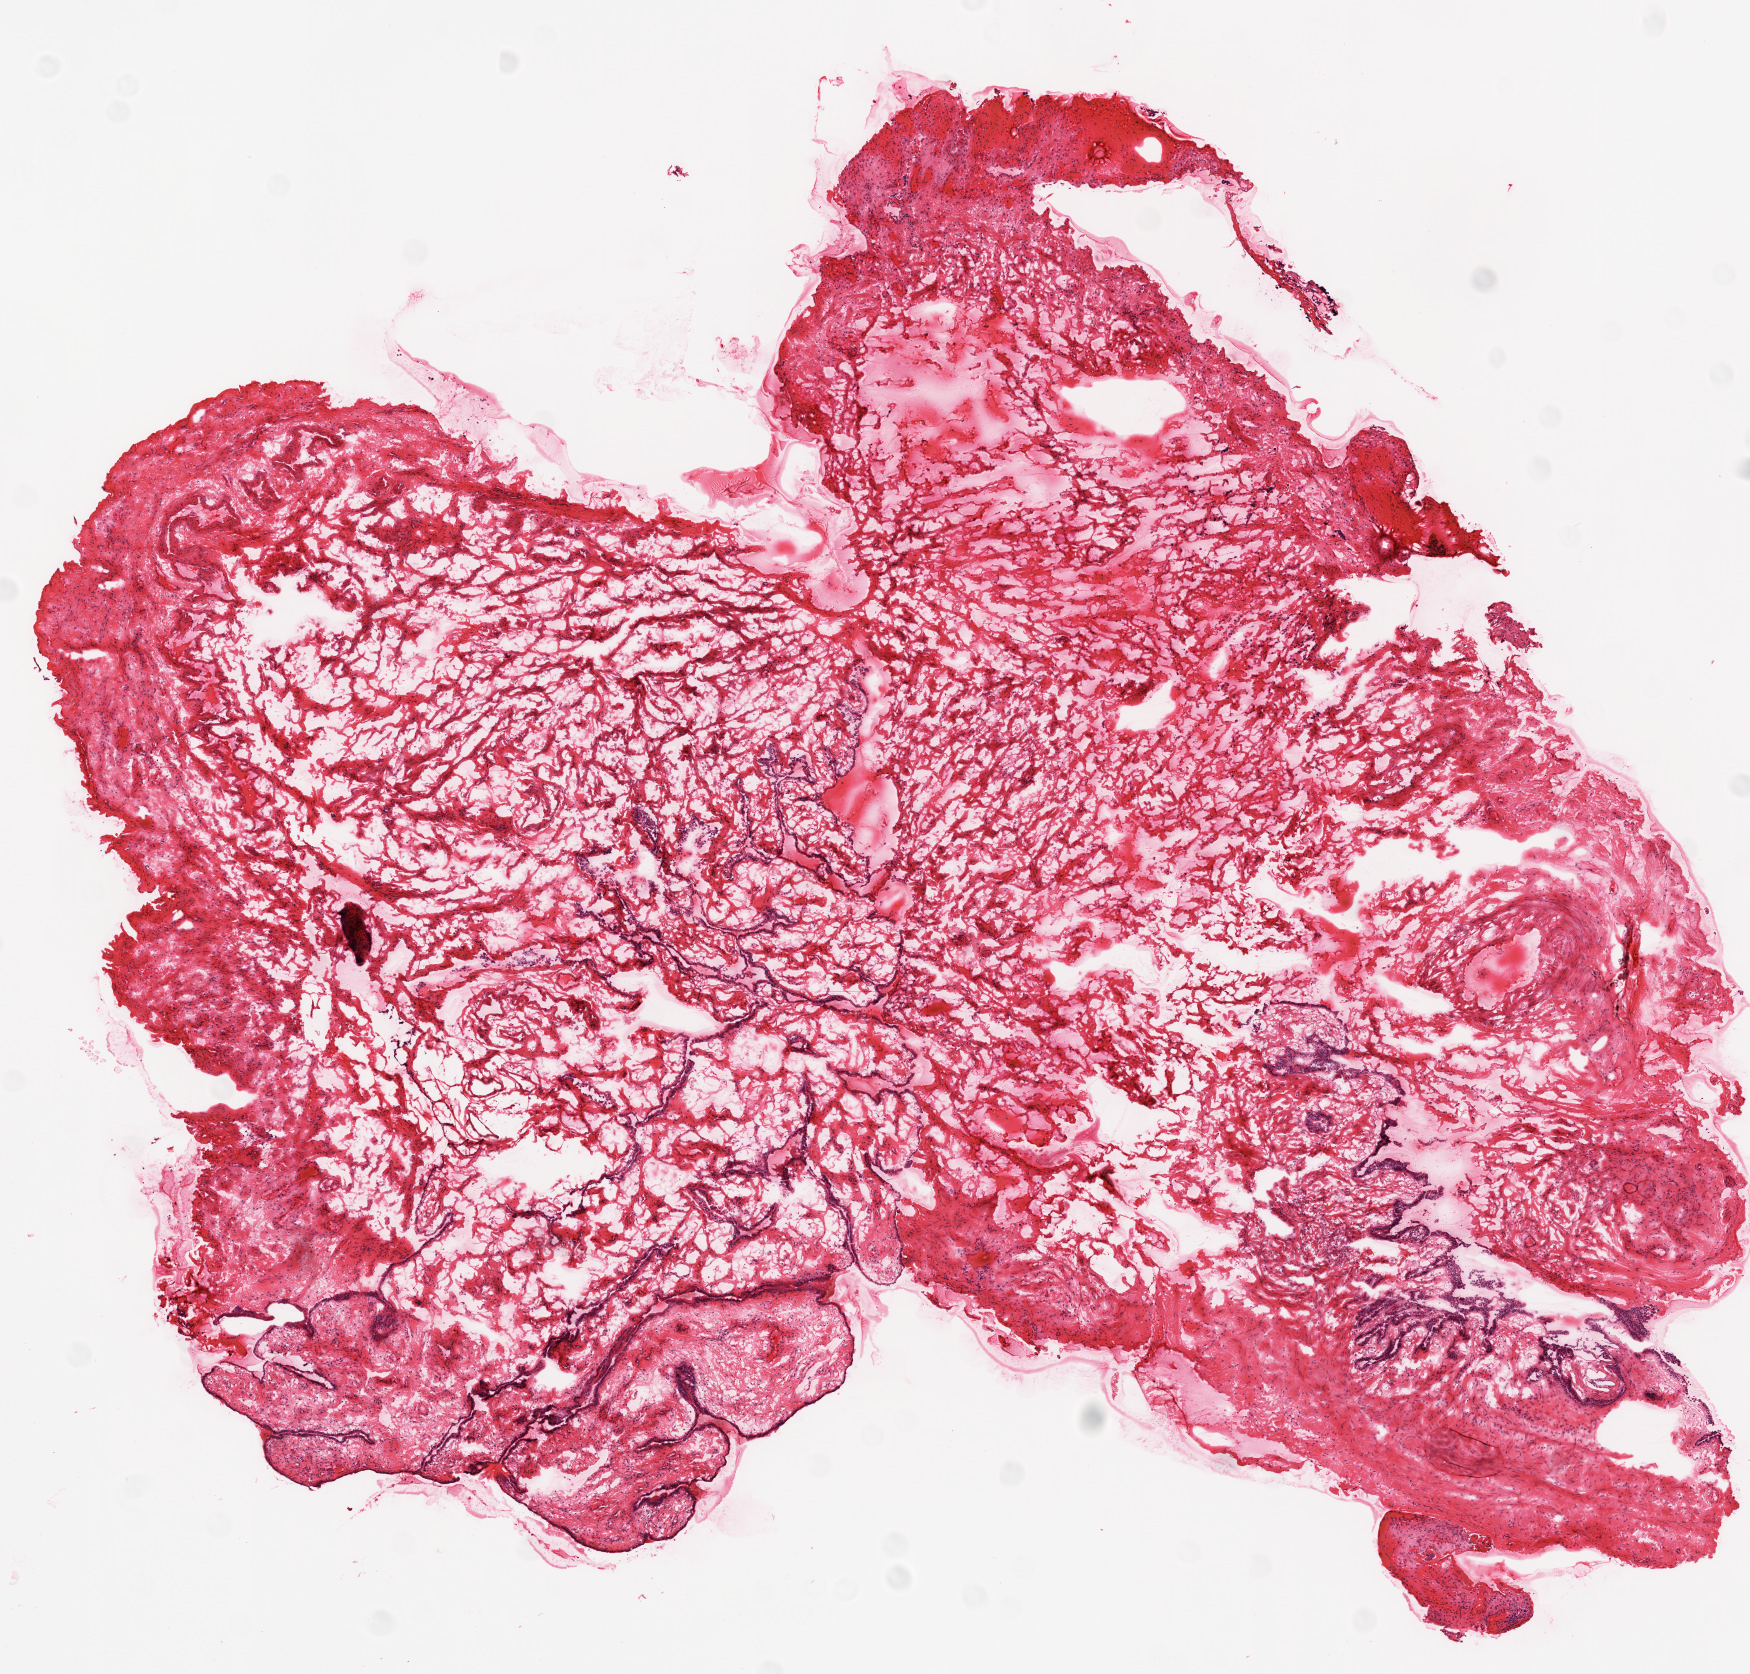
Digitized H&E tissue section (whole slide), shown as a low-resolution overview of the whole scanned area (about 7.0 x 6.7 mm); frozen section; ovary, solid tissue normal (non-tumour tissue) sample. Female, age 76 years at initial diagnosis.
- this section: solid tissue normal (non-tumour) sample from the same patient
- patient diagnosis: Serous cystadenocarcinoma, NOS